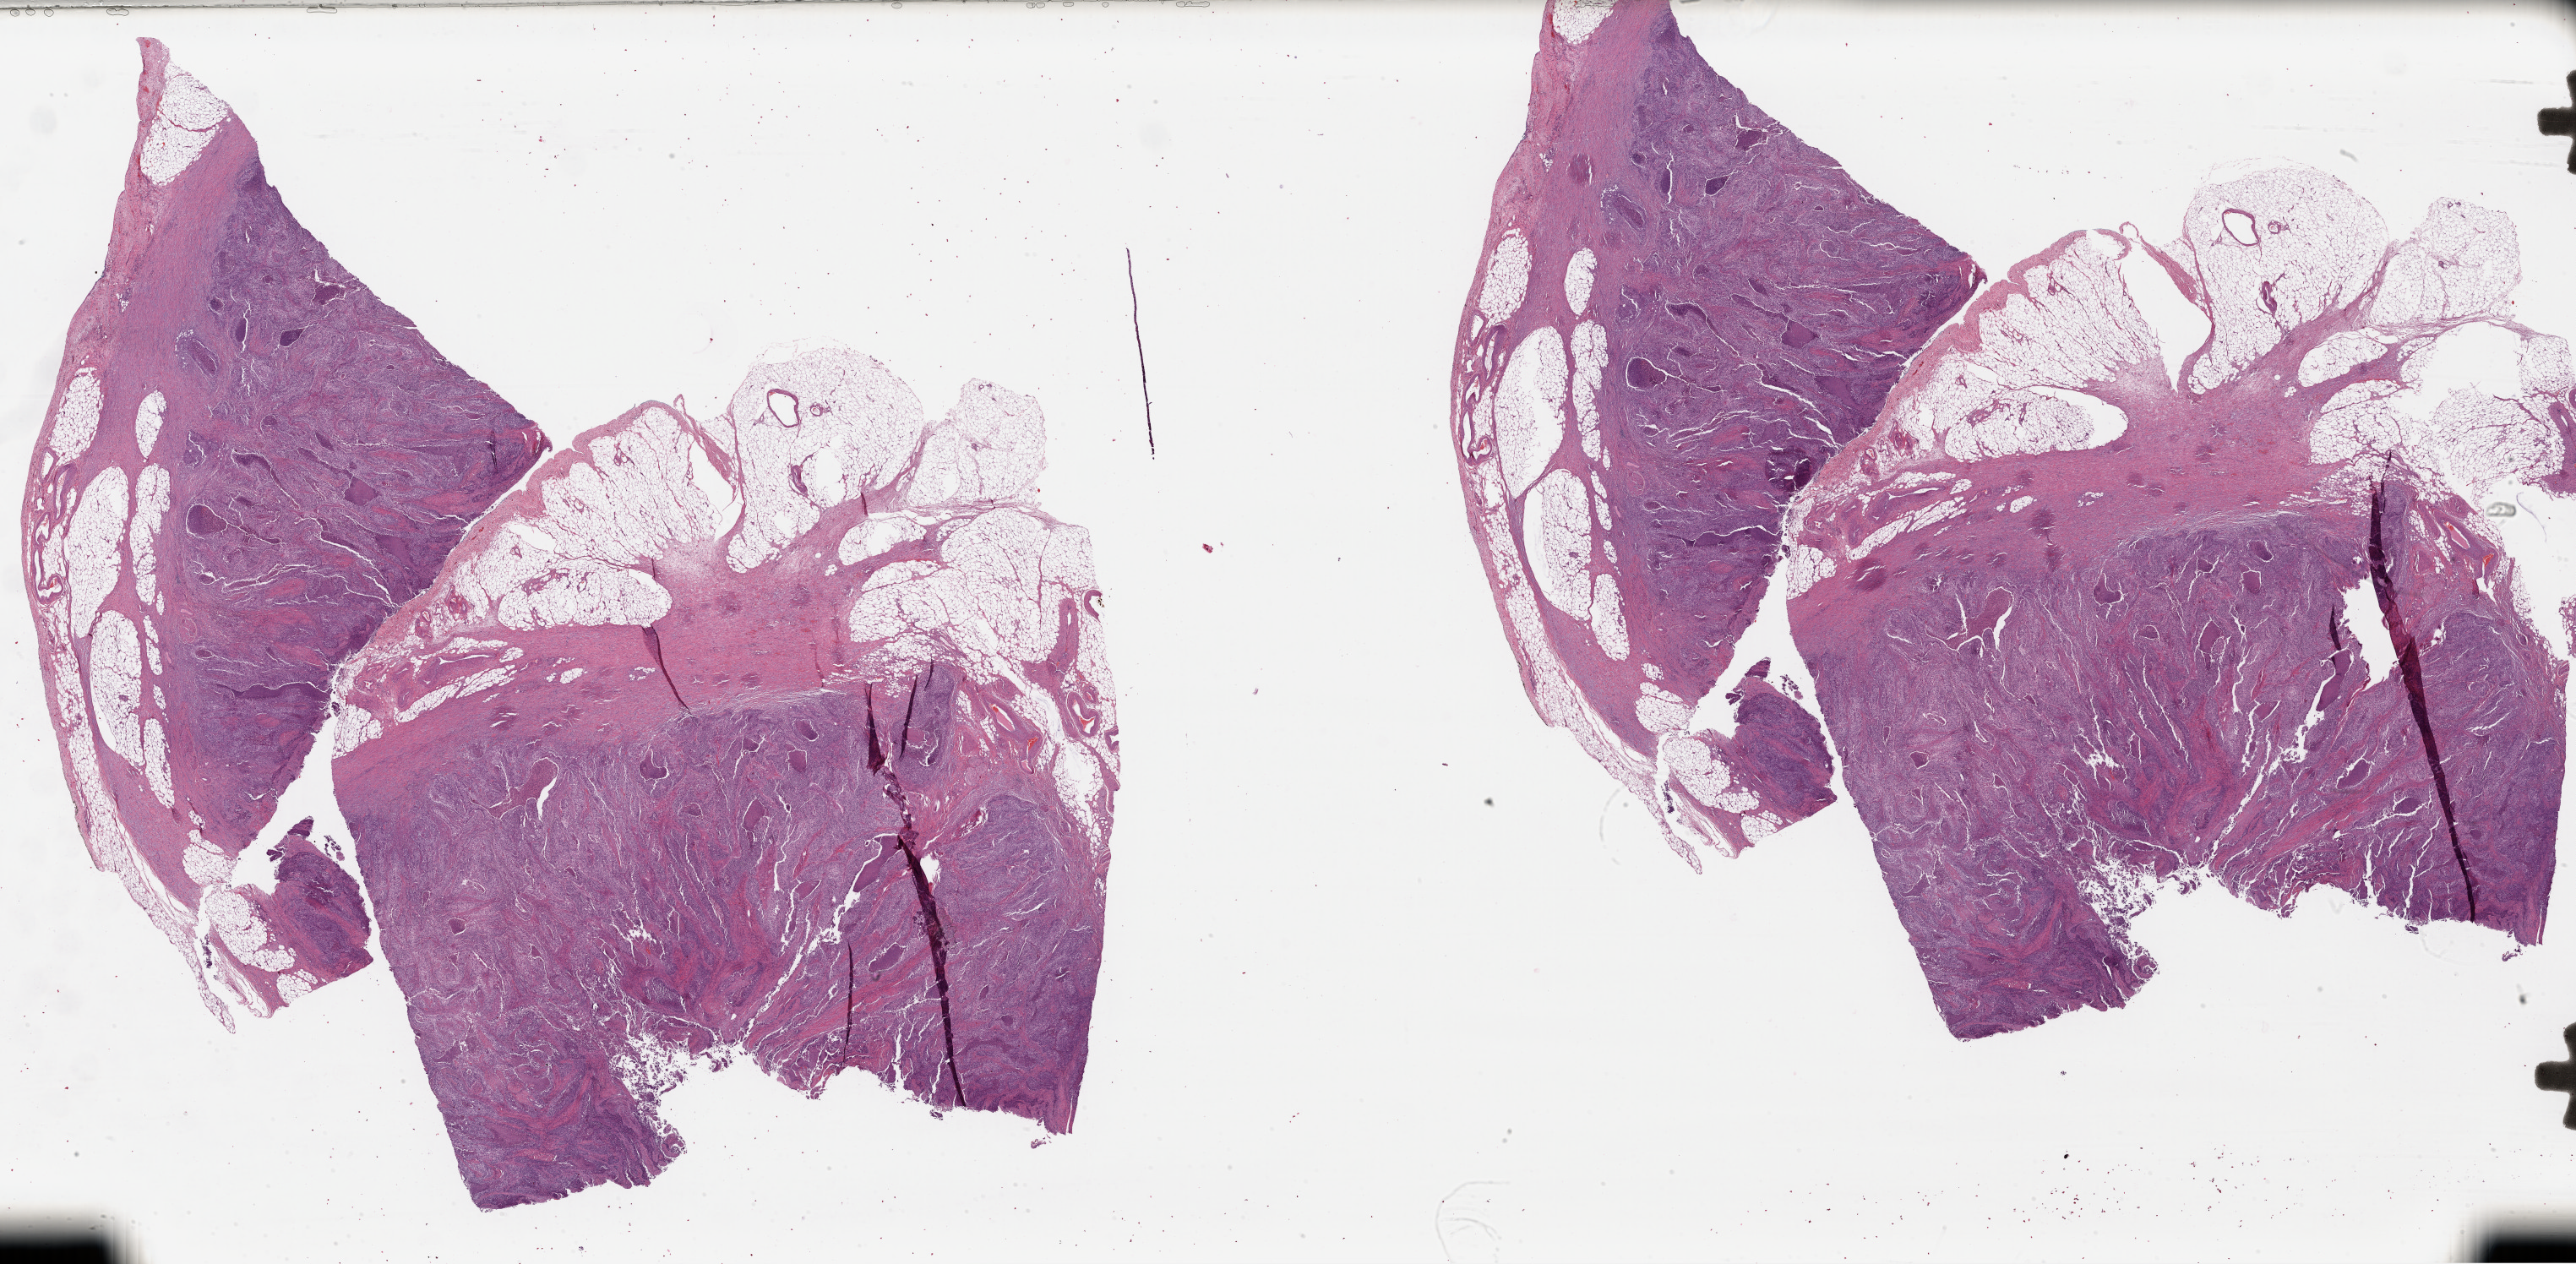
Whole-slide histology image, H&E — shown as a low-resolution overview of the whole scanned area (about 47.9 x 23.5 mm, acquisition: 40x scan). Formalin-fixed paraffin-embedded (FFPE) diagnostic section. Sample: primary tumour, bladder. Female patient; age at initial diagnosis 77 years. Histologic grade: high grade.
* pathologic diagnosis: Transitional cell carcinoma
* AJCC pathologic stage: II